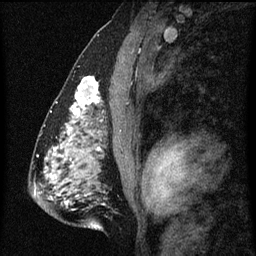
Breast MRI (dynamic contrast-enhanced), one sagittal slice; slice 35 of 60 in the series (ordered by position); dynamic contrast-enhanced series, image 2 of 3 at this slice position (ordered by acquisition); 1.5 T; TE 4.2 ms, TR 8 ms; 2 mm slice thickness; 256 × 256 image matrix, field of view 180 × 180 mm. Female patient, age 51 years.
Structures marked on this image (semi-automatic segmentation, software-assisted and operator-edited):
- analysis volume of interest (the breast-tissue region the enhancement analysis was run in; not a lesion): bounding box [x1, y1, x2, y2] px = [64, 78, 102, 129]
- tumour enhancement mask (voxels above the 70 % enhancement threshold inside the analysis volume of interest): [70, 78, 102, 123]